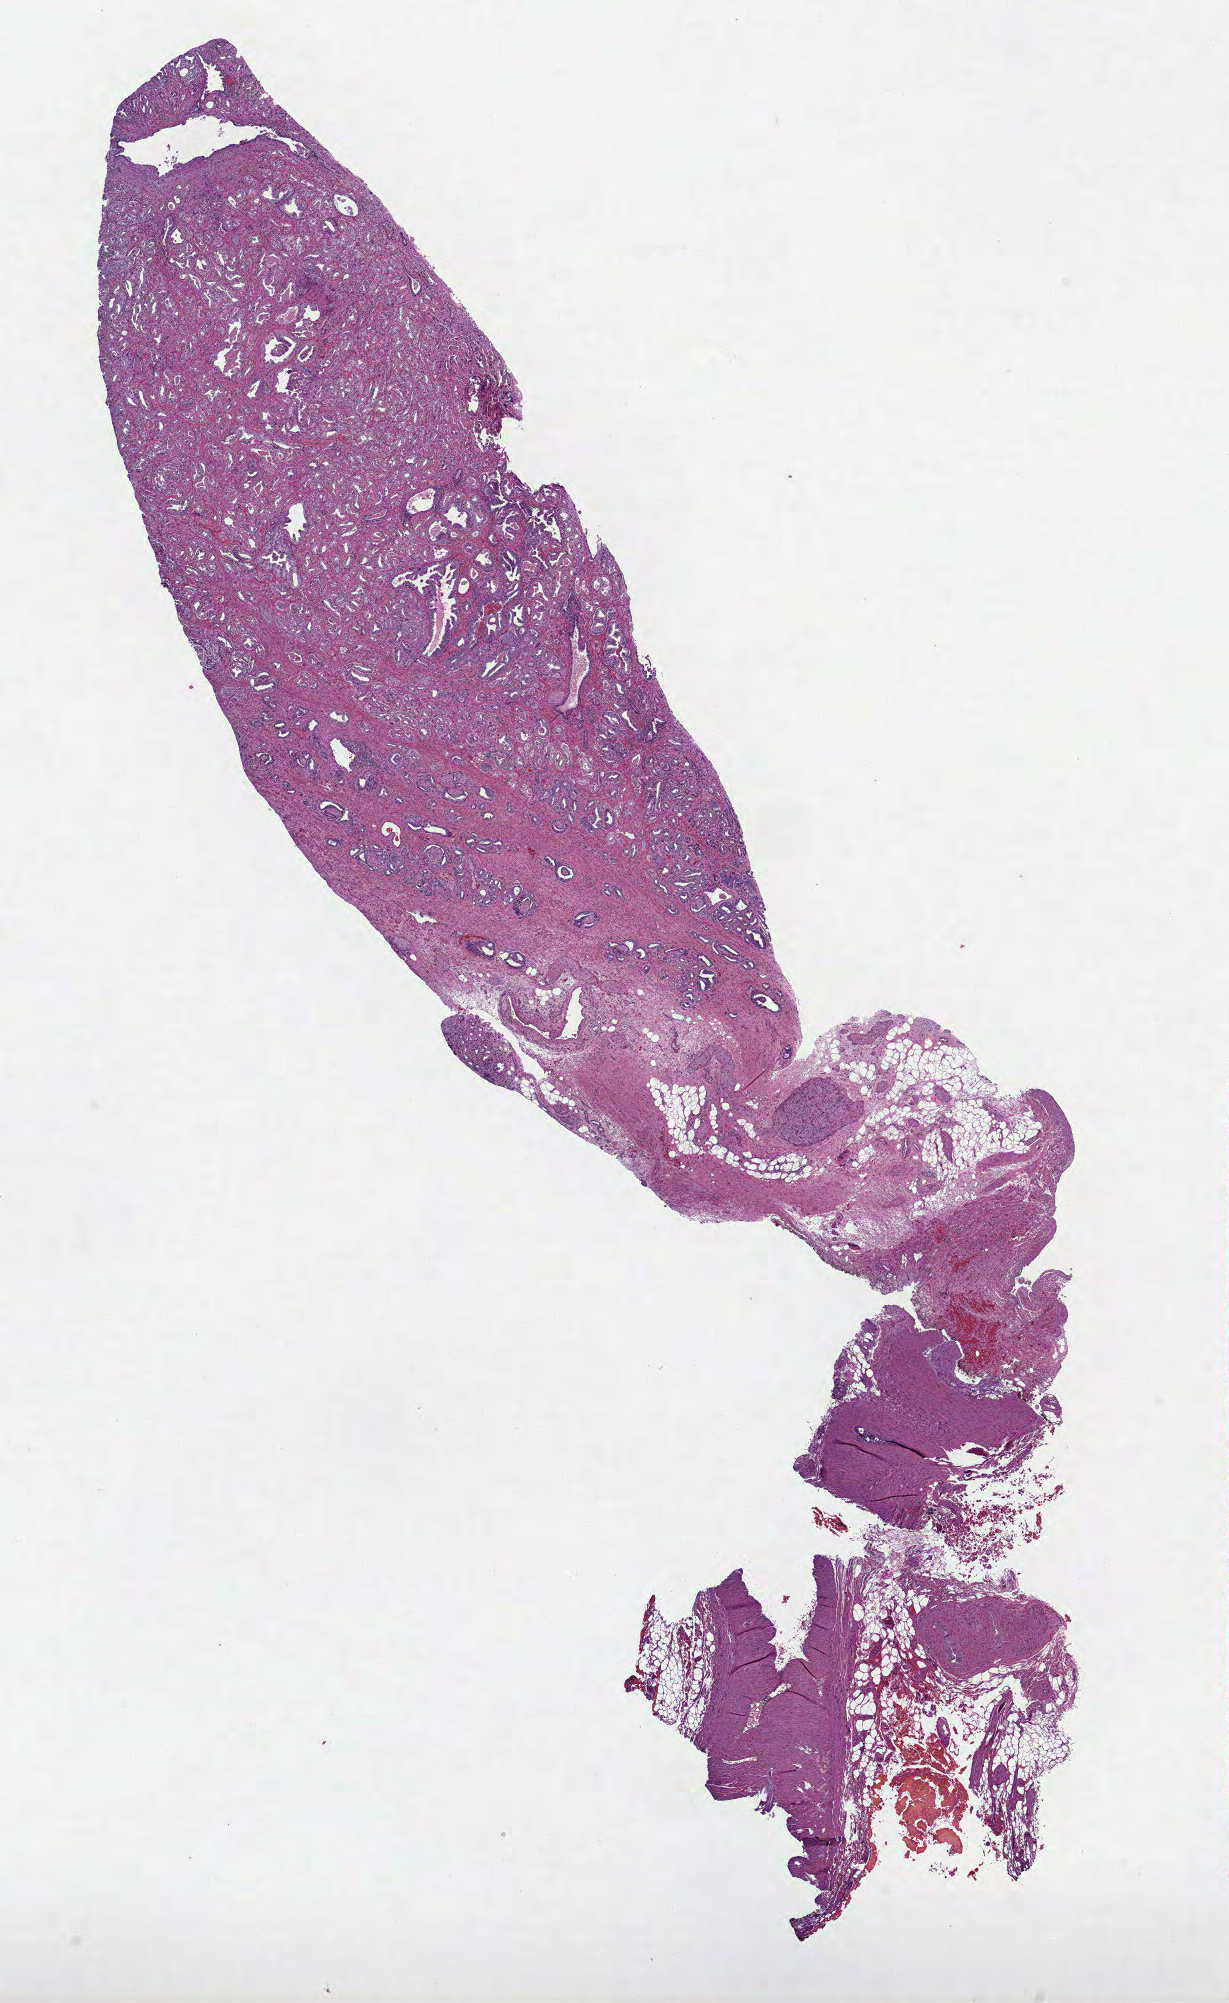
H&E-stained whole-slide image — a low-resolution overview of the entire scanned area, about 9.9 x 16.2 mm (slide scanned at 40x), formalin-fixed paraffin-embedded (FFPE) diagnostic section, prostate, primary tumour sample. Male, age 64 years at initial diagnosis. Gleason score: 7 (3+4).
Lymph nodes positive (case pathology): 0 of 3 examined. Histologic diagnosis: Adenocarcinoma, NOS. Laterality: bilateral.